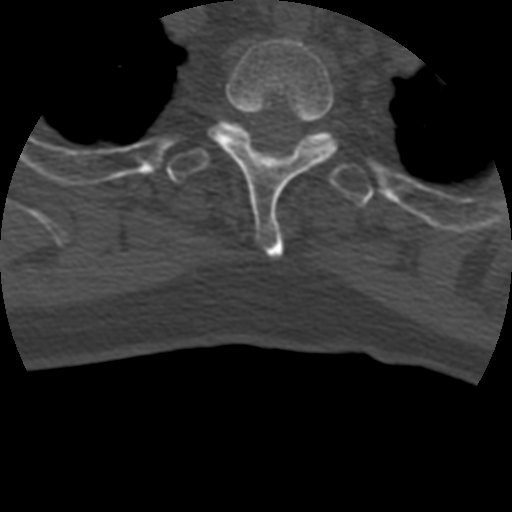
CT including the spine, one axial slice. Position 364 of 399 along the scan axis. Reconstruction kernel STANDARD. Bone window (W 1800 / L 400 HU). 512 × 512 image matrix, field of view 160 × 160 mm. Patient age 69 years. From the clinical record (not read from this slice): primary cancer: prostate.
Structures marked on this image (semi-automatic segmentation, software-assisted and operator-edited):
- T2 vertebra: bounding box (x1, y1, x2, y2) in pixels: (209, 39, 338, 258)
- T3 vertebra: (167, 121, 374, 208)